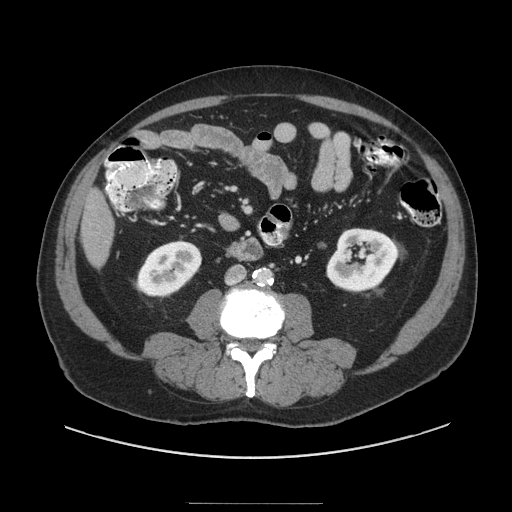
Contrast-enhanced abdominal CT (liver protocol), one axial slice. Slice 18 of 91 in the series (ordered by position). Reconstruction kernel STANDARD. 140 kVp. Soft-tissue window (W 400 / L 40 HU). 2.5 mm slice thickness. 512 × 512 image matrix. Case-level facts recorded for this patient, not image findings: diagnosis: hepatocellular carcinoma (patient treated with transarterial chemoembolisation; whether this scan precedes or follows treatment is not stated here); TNM stage (as recorded): Stage-I; Child-Pugh class: A; tumour differentiation: well differentiated; tumour nodularity: uninodular.
Outlined on this slice (semi-automatically segmented with operator editing):
- liver parenchyma outside the tumour (the mass and vessels are separate outlines, so this box may not span the whole liver): bounding box <80,189,114,266> (left, top, right, bottom; pixels)